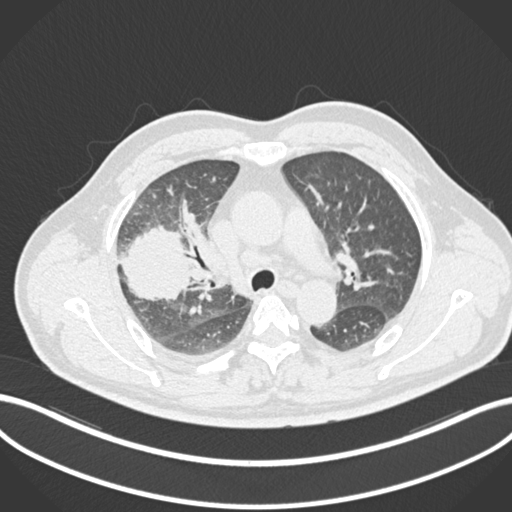
Chest CT, one axial slice. Slice 655 of 852 in the series (ordered by position). Reconstruction kernel B30f. 120 kVp. Lung window (W 1500 / L -600 HU). 512 × 512 image matrix, field of view 400 × 400 mm. Patient: male, 55 years. From the clinical record (not read from this slice): clinical TNM (as recorded): T3 N2 M1.
Outlined on this slice (bounding box drawn by a radiologist):
- lung tumour (recorded histology: adenocarcinoma): box from (x=116, y=224) to (x=197, y=301) px